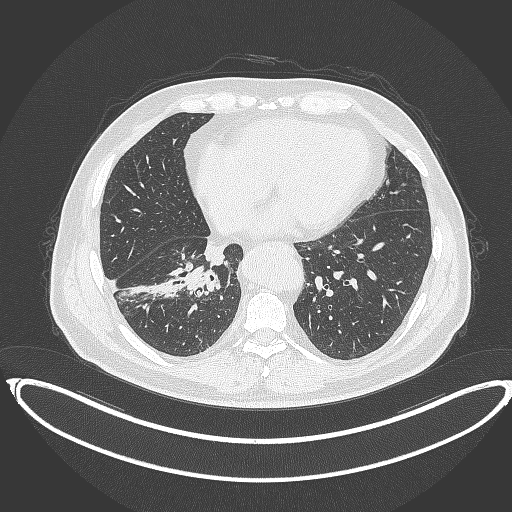
Chest CT, one axial slice. Position 147 of 387 along the scan axis. 120 kVp. Lung window (W 1500 / L -600 HU). 512 × 512 image matrix, field of view 448 × 448 mm. Patient: male, 61 years. From the clinical record (not read from this slice): clinical TNM (as recorded): T1b N1 M0.
Annotated regions visible in this slice (rectangle marked by the reading radiologist):
- lung tumour (recorded histology: squamous cell carcinoma): box from (x=182, y=261) to (x=223, y=297) px